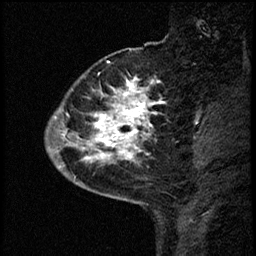
Breast MRI (dynamic contrast-enhanced), one sagittal slice. Slice 14 of 68 in the series (ordered by position). Dynamic contrast-enhanced study with each time point stored as its own series, time point 2 of 3 at this slice position (early post-contrast, ordered by acquisition time). 1.5 T. TE 4.2 ms, TR 17.6 ms. 256 × 256 image matrix, field of view 200 × 200 mm. Patient: female, 52 years. From the clinical record (not read from this slice): setting: breast cancer imaged before/during neoadjuvant chemotherapy; receptor status: HER2-positive.
Outlined on this slice (semi-automatic segmentation, software-assisted and operator-edited):
- analysis volume of interest (the breast-tissue region the enhancement analysis was run in; not a lesion): bounding box <50,61,165,184> (left, top, right, bottom; pixels)
- tumour enhancement mask (voxels above the 100 % enhancement threshold inside the analysis volume of interest): <55,79,159,168>